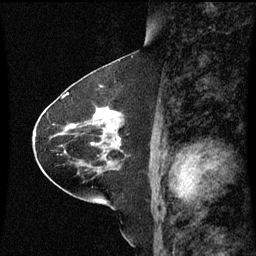
Breast MRI (dynamic contrast-enhanced), one sagittal slice; slice 34 of 60 in the series (ordered by position); dynamic contrast-enhanced series, image 2 of 3 at this slice position (ordered by acquisition); 1.5 T; TE 4.2 ms, TR 8.9 ms; 2 mm slice thickness; 256 × 256 image matrix, field of view 200 × 200 mm. Female patient, age 63 years. From the clinical record (not read from this slice): setting: breast cancer imaged before/during neoadjuvant chemotherapy; receptor status: HR-positive, HER2-negative.
Structures marked on this image (semi-automatic segmentation, software-assisted and operator-edited):
- analysis volume of interest (the breast-tissue region the enhancement analysis was run in; not a lesion): bounding box <77,108,125,151> (left, top, right, bottom; pixels)
- tumour enhancement mask (voxels above the 70 % enhancement threshold inside the analysis volume of interest): <94,110,120,141>